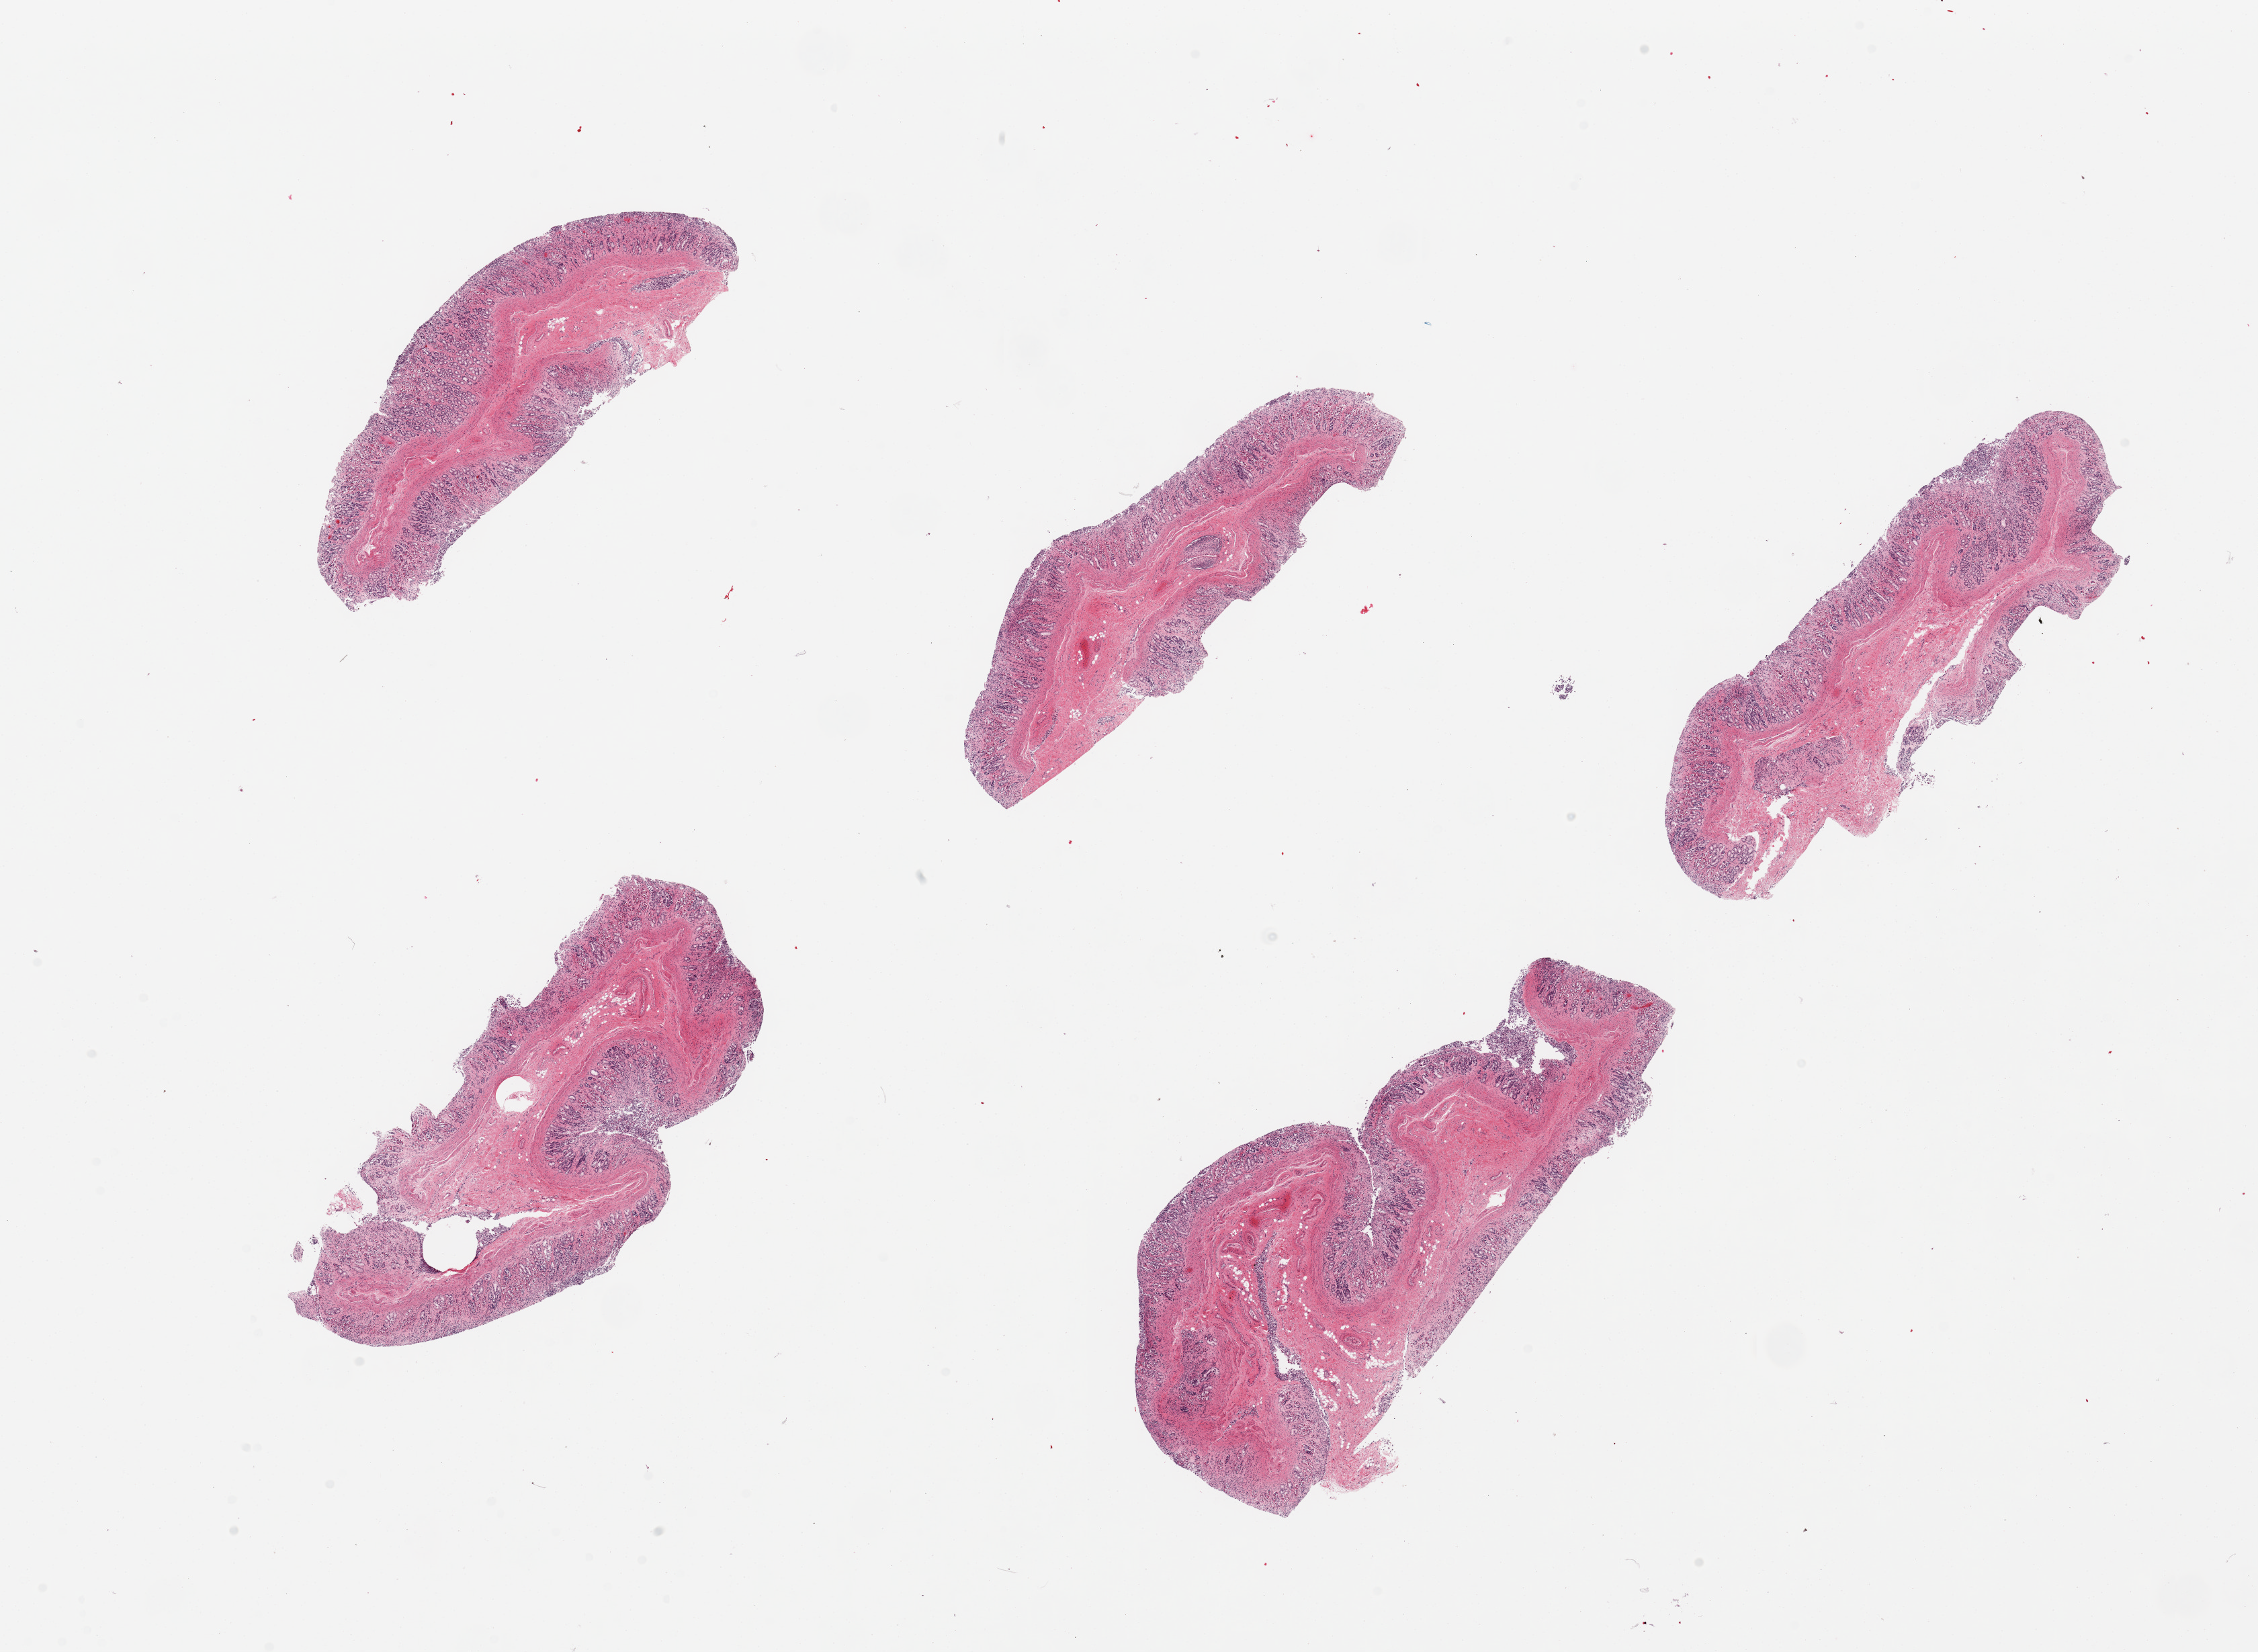
Haematoxylin and eosin whole-slide image, a low-resolution overview of the entire scanned area, about 26.6 x 19.4 mm; PAXgene-fixed, paraffin-embedded tissue; sampled site (target tissue): transverse colon; donor tissue sample. Donor sex: male.
Reviewer comment on this tissue sample: 6 pieces; mucosa up to ~0.5mm thick but completely autolyzed.